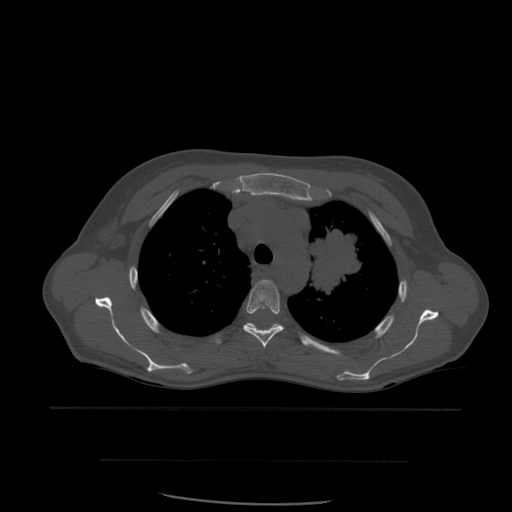
CT including the spine, one axial slice; slice 425 of 574 in the series (ordered by position); bone window (W 1800 / L 400 HU); 1.25 mm slice thickness; 512 × 512 image matrix, field of view 392 × 392 mm. Patient age 48 years. Case-level facts recorded for this patient, not image findings: primary cancer: lung; vertebrae with lytic lesions (as recorded): T11.
Outlined on this slice (semi-automatically segmented with operator editing):
- T4 vertebra: bounding box <243,280,284,349> (left, top, right, bottom; pixels)
- T5 vertebra: <246,323,305,346>